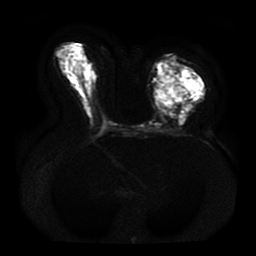
Breast MRI, one axial slice. Position 21 of 41 along the scan axis. Diffusion-weighted series; image 2 of 4 stored at this slice position (different b-values; order by instance number). 1.5 T. 5 mm slice thickness. 256 × 256 image matrix, field of view 330 × 330 mm. Female patient.
Outlined on this slice (expert manual segmentation):
- tumour on diffusion-weighted imaging: bounding box <161,69,202,101> (left, top, right, bottom; pixels)